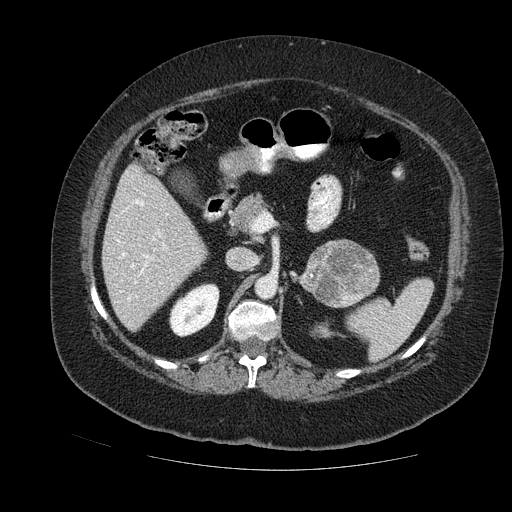
Contrast-enhanced abdominal CT, one axial slice. Slice 68 of 121 in the series (ordered by position). Soft-tissue window (W 400 / L 40 HU). 2.5 mm slice thickness. 512 × 512 image matrix, field of view 420 × 420 mm. Female patient. Case-level facts recorded for this patient, not image findings: diagnosis: adrenocortical carcinoma; tumour side: left adrenal.
Annotated regions visible in this slice (semi-automatic segmentation, software-assisted and operator-edited):
- mass: bounding box [x1, y1, x2, y2] px = [303, 239, 379, 307]